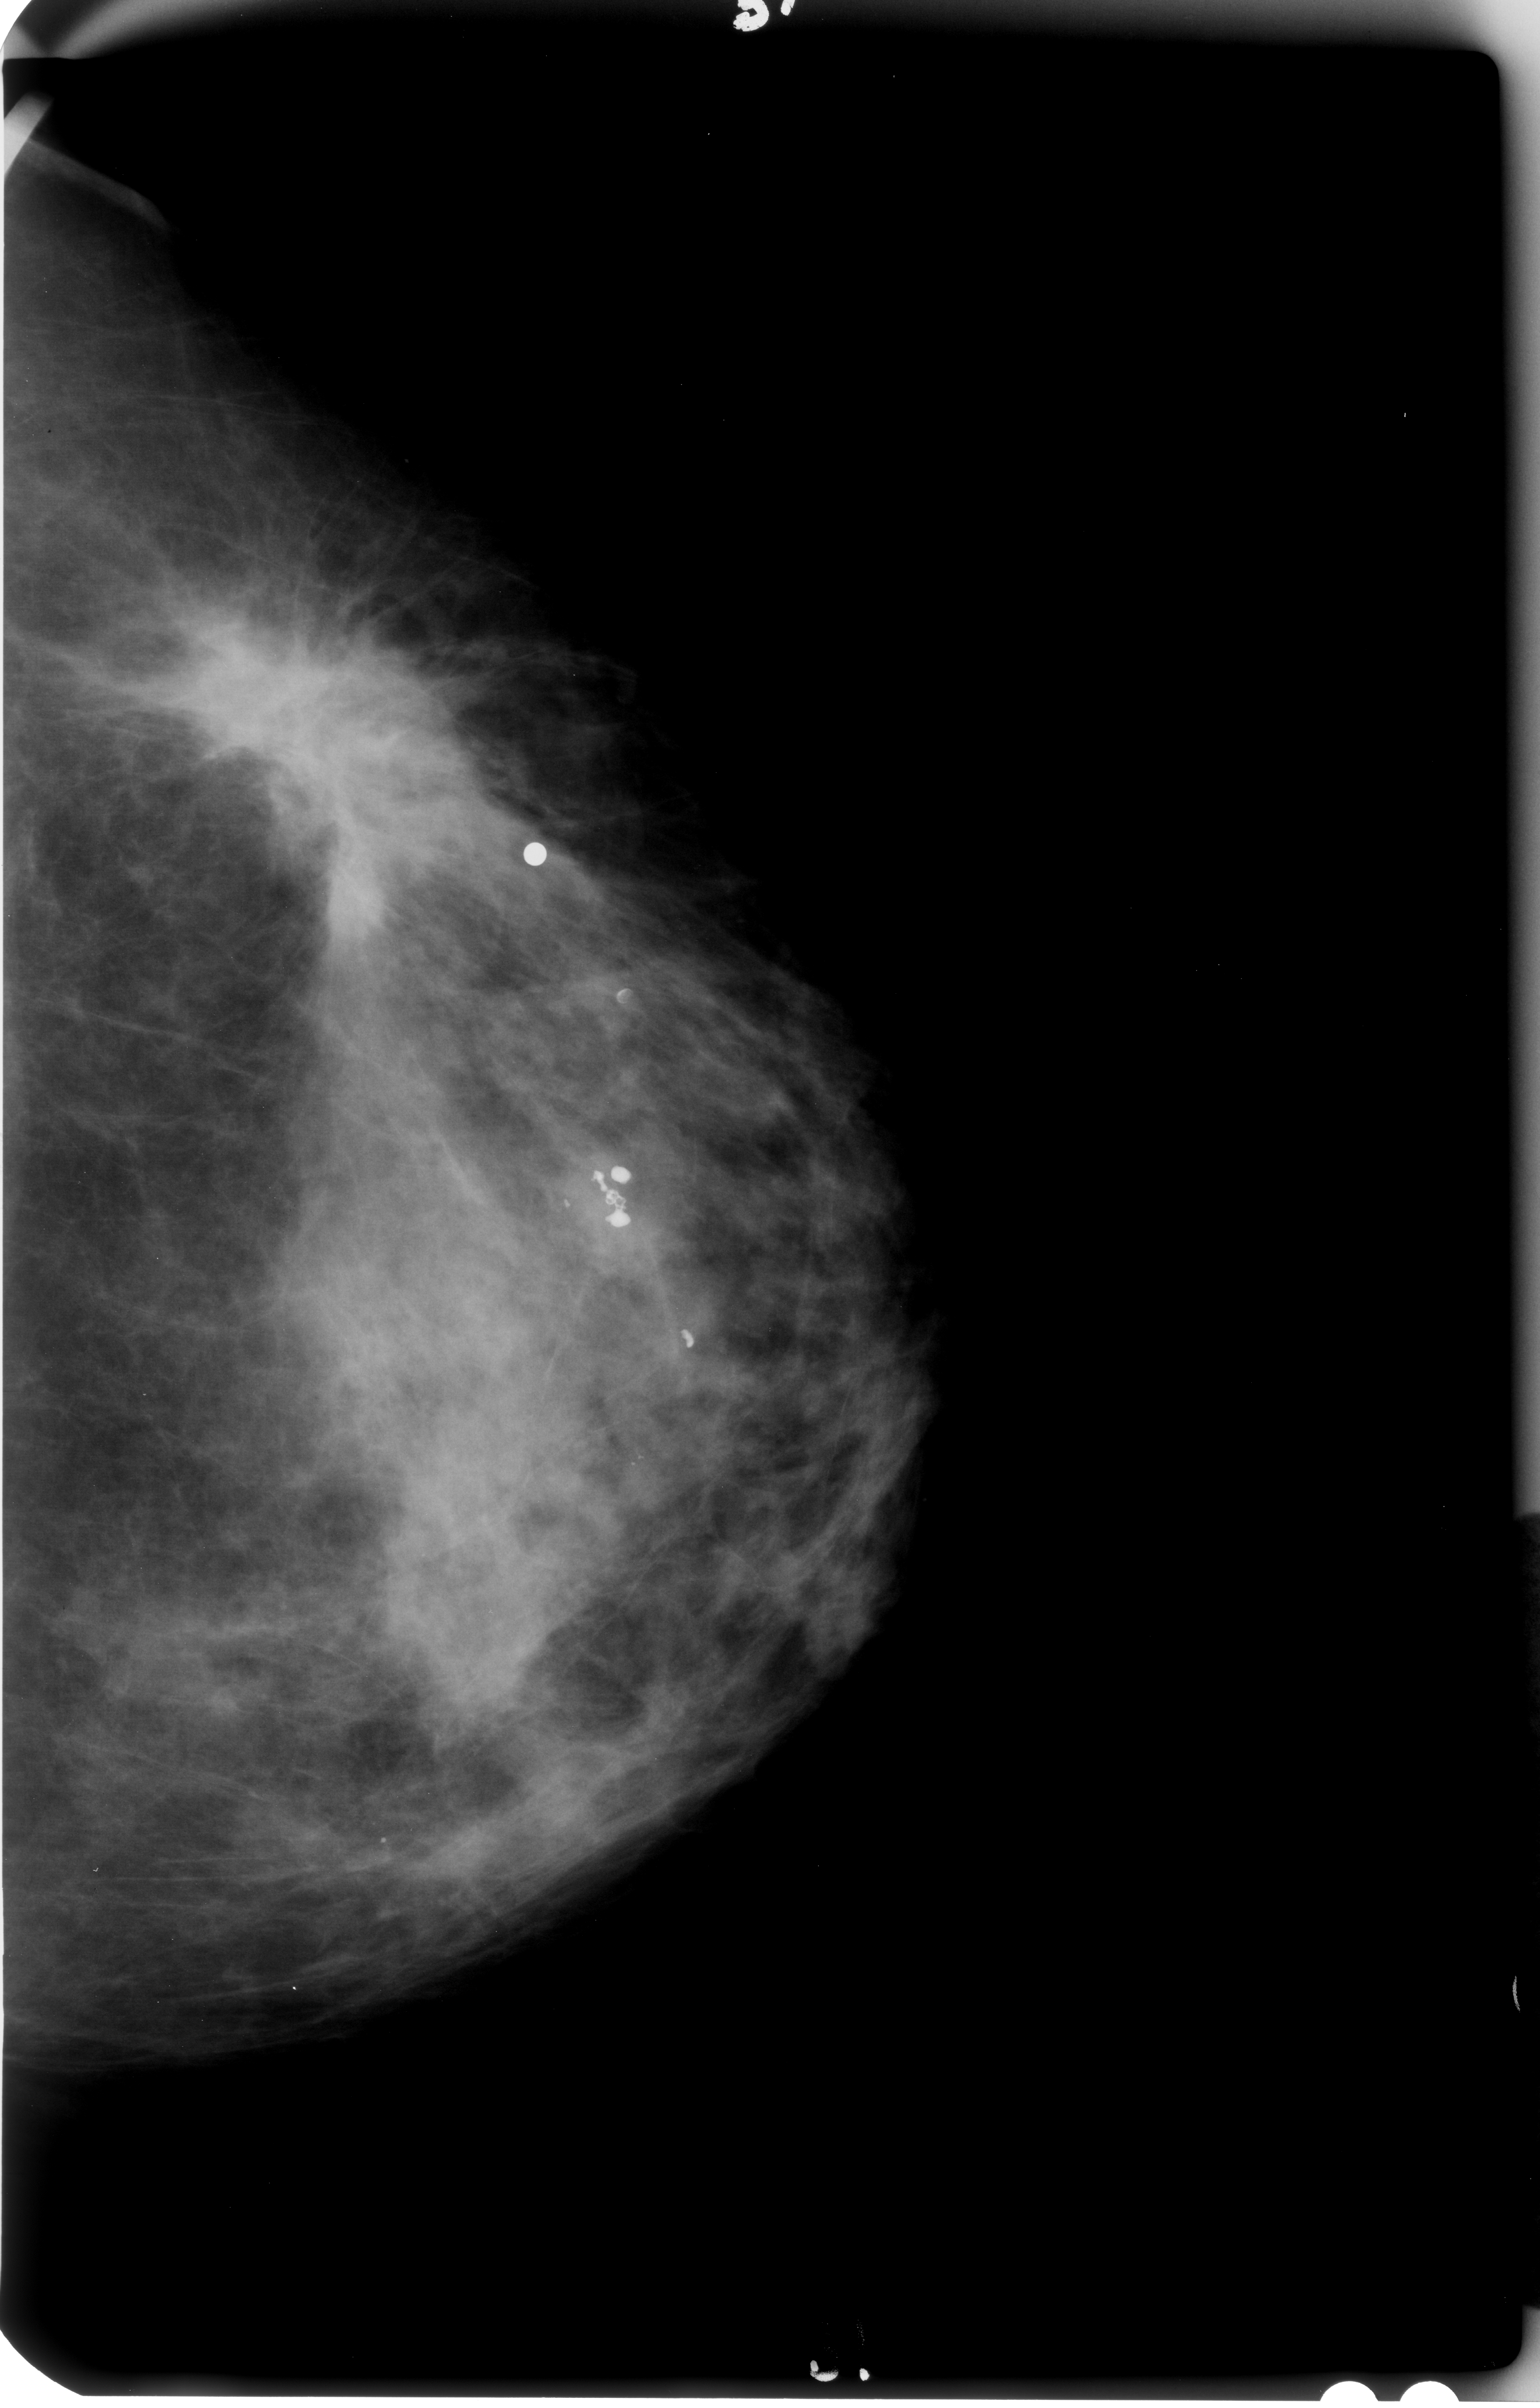
Mammogram (digitized film), left breast, CC view, BI-RADS breast density category 4 (scale 1–4).
- Mass, shape irregular / architectural distortion, margins ill defined / spiculated; BI-RADS assessment category 4; subtlety rating 4 on a 1 (subtle) to 5 (obvious) scale; pathology (as recorded): malignant.